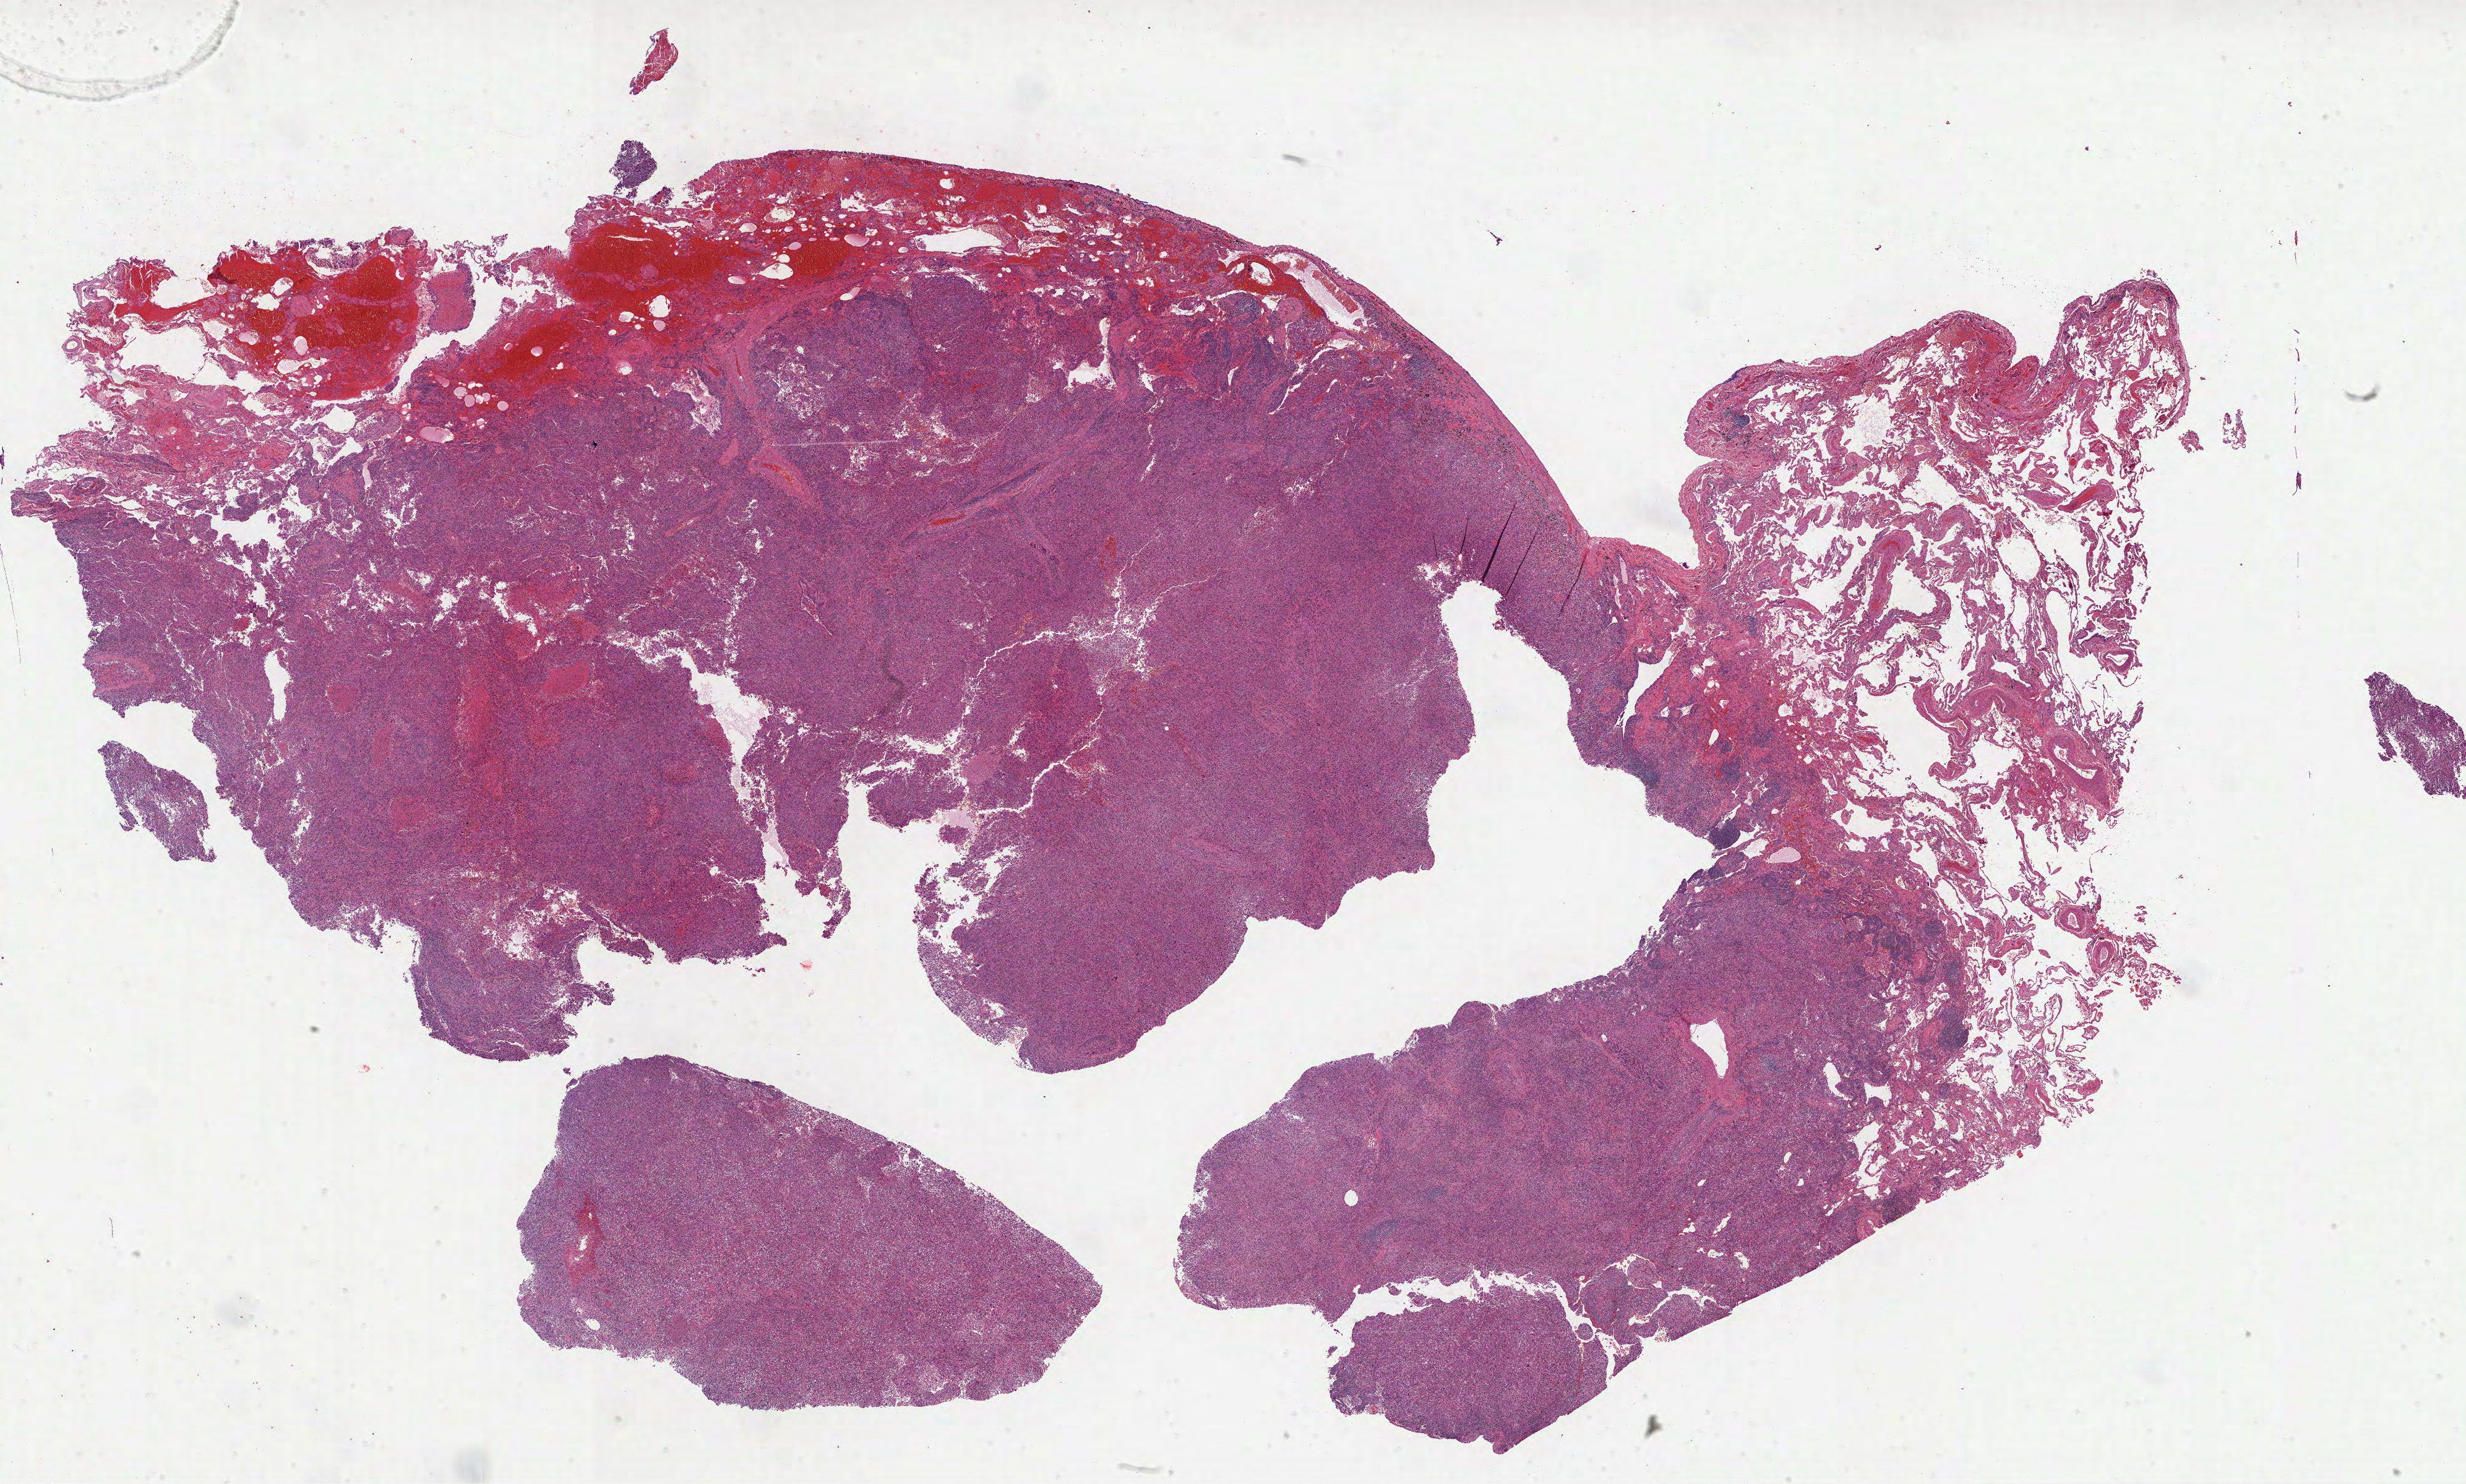
Whole-slide histology image, H&E, shown as a low-resolution overview of the whole scanned area (about 32.1 x 19.3 mm). Formalin-fixed paraffin-embedded (FFPE) diagnostic section. Primary tumour sample from the lung. Patient: male, age at initial diagnosis 72 years.
Pathologic diagnosis: Adenocarcinoma with mixed subtypes.